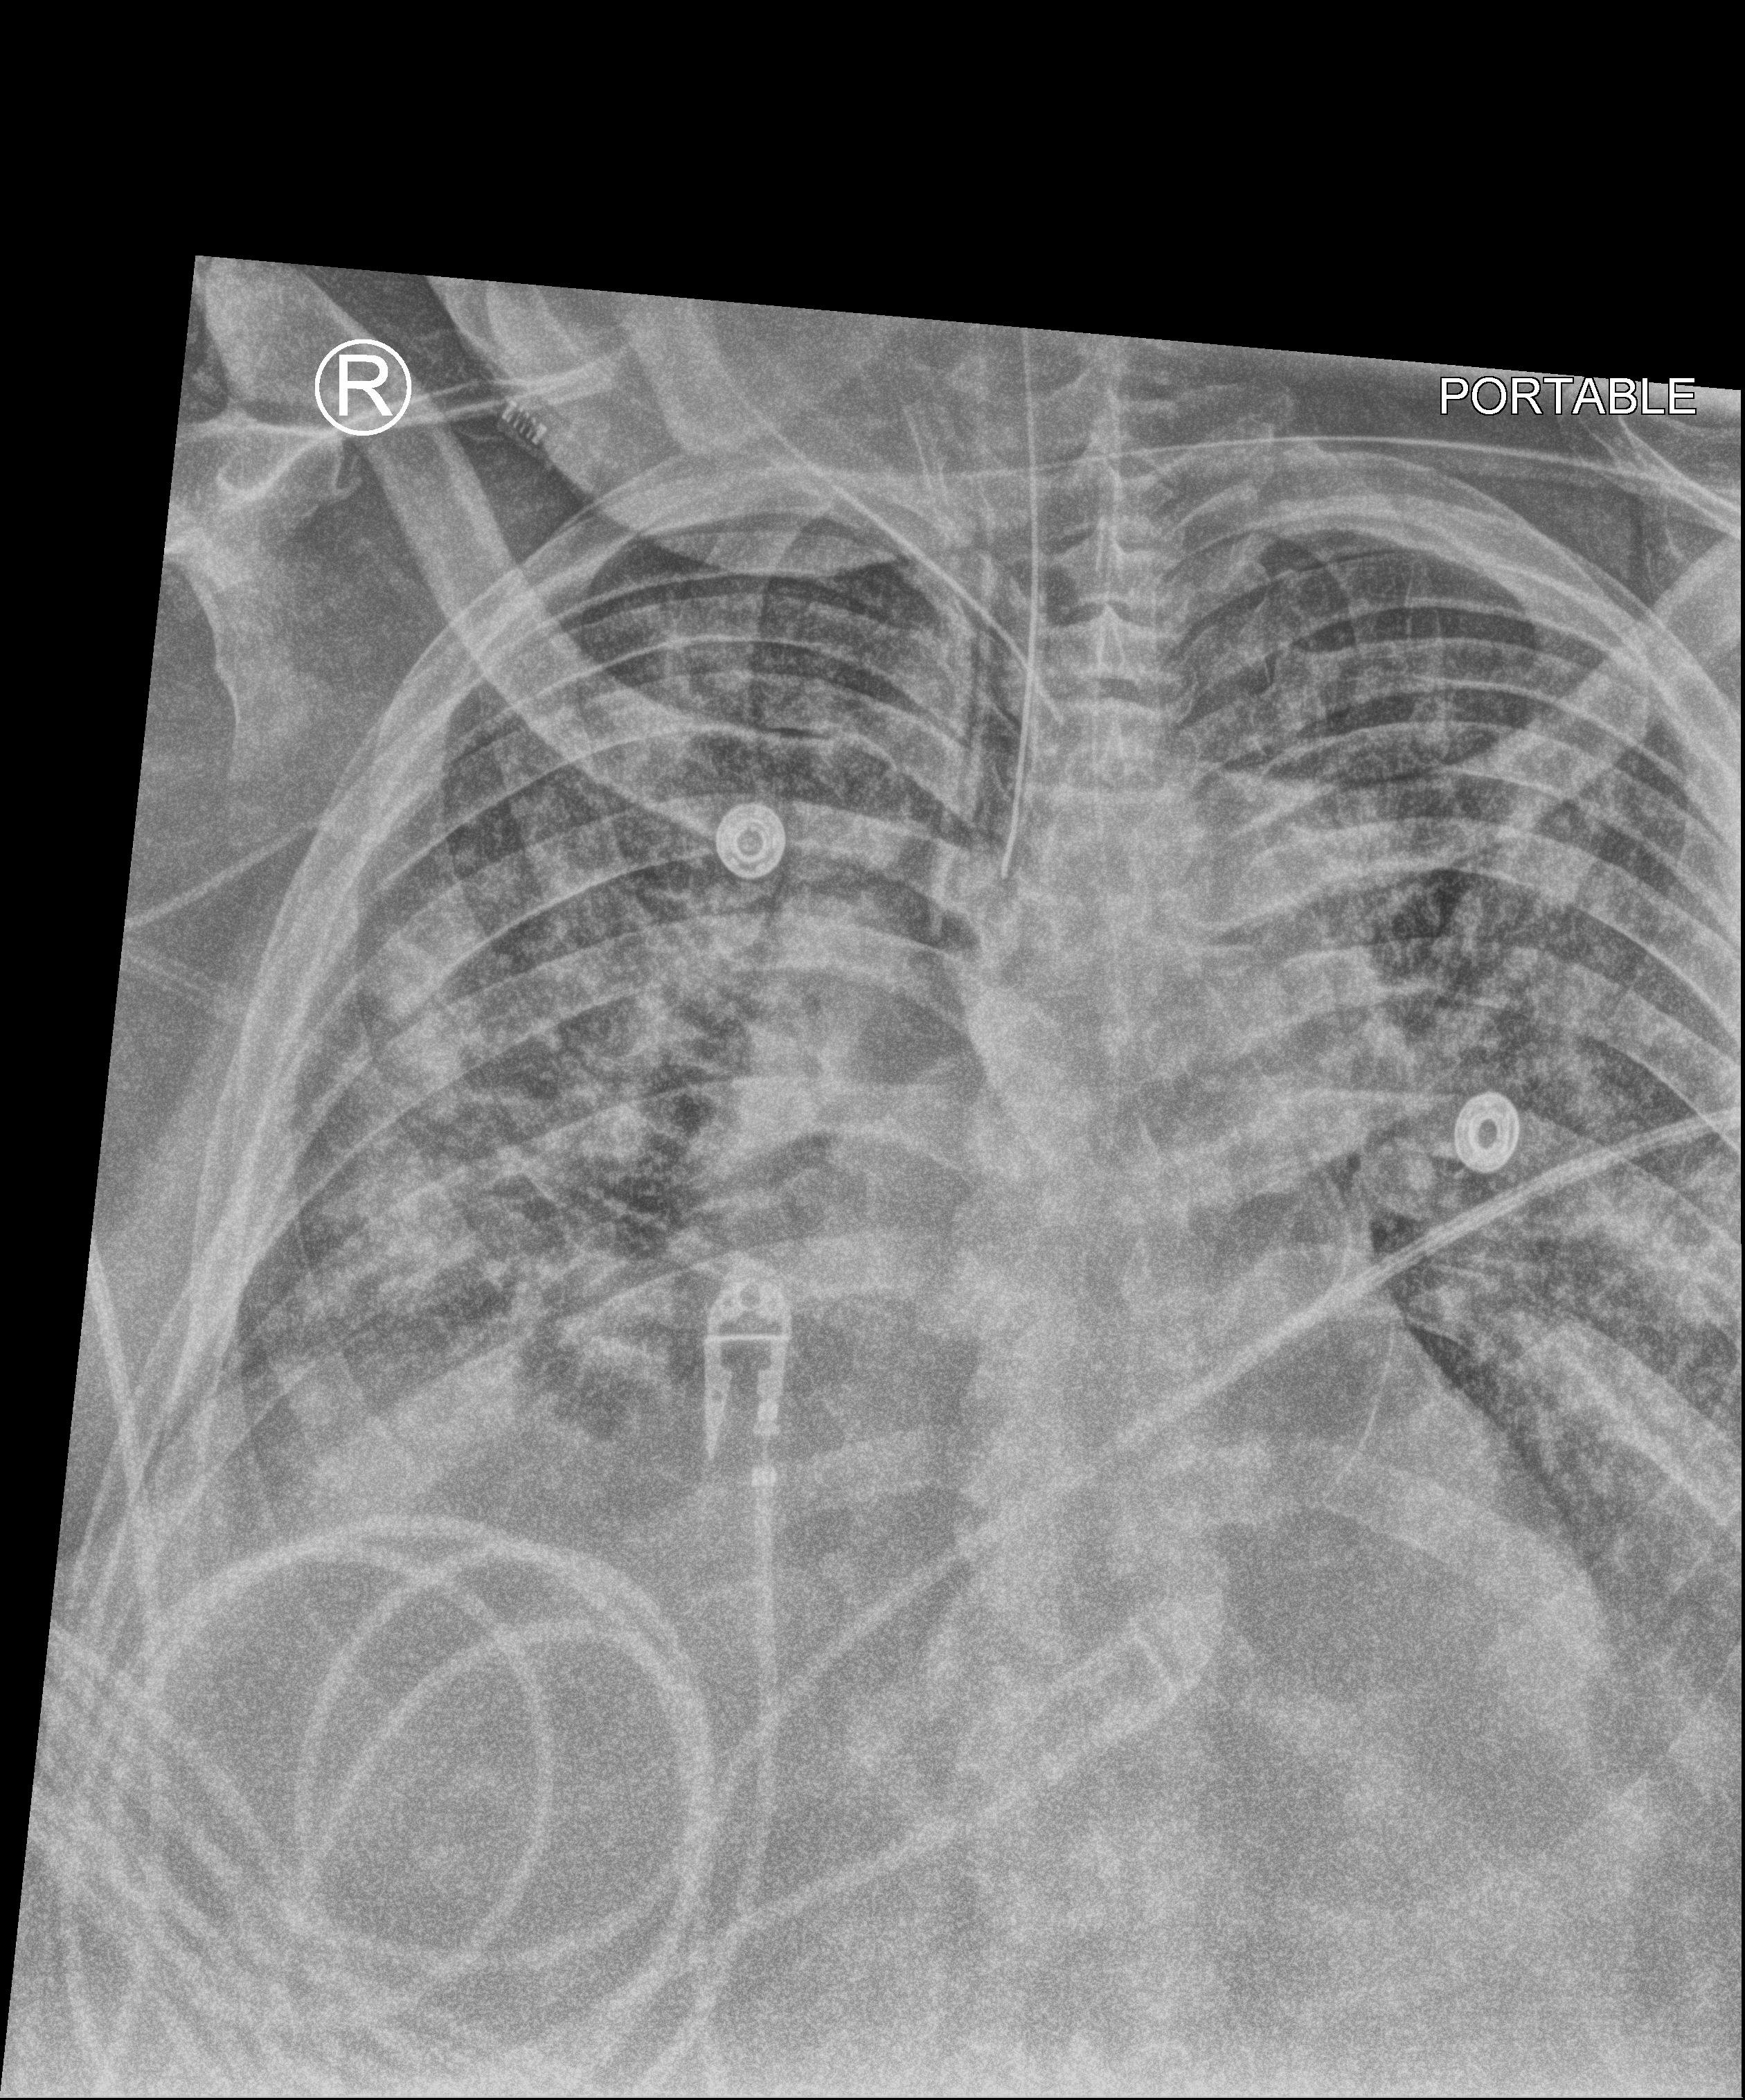
Chest X-ray (portable), anteroposterior (AP) projection. Male patient hospitalised with COVID-19, age 60–74 years.
From the hospital-stay record, not from the radiograph (when in the stay this image was taken is not recorded):
- admitted to intensive care during this hospital stay: yes
- mechanically ventilated during this hospital stay: yes